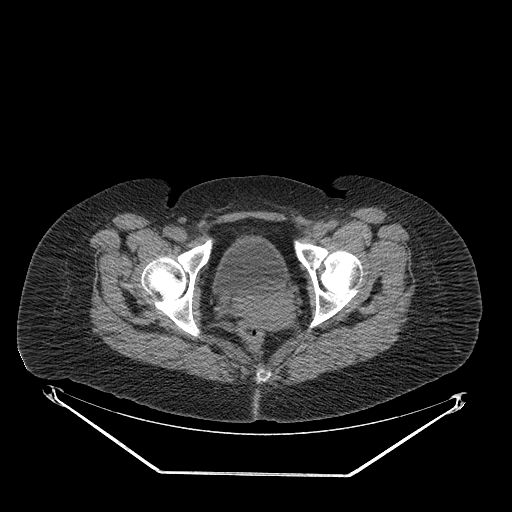
CT of an extremity soft-tissue mass (from a PET/CT study), one axial slice. Position 60 of 267 along the scan axis. 140 kVp. Soft-tissue window (W 400 / L 40 HU). 512 × 512 image matrix. Female patient. From the clinical record (not read from this slice): histological type: myxofibrosarcoma; grade: intermediate; site of the primary tumour: left thigh.
Structures marked on this image (expert contour drawn on MRI and transferred to this co-registered scan by the dataset authors):
- gross tumour volume including surrounding oedema: bounding box [x1, y1, x2, y2] px = [301, 228, 348, 248]